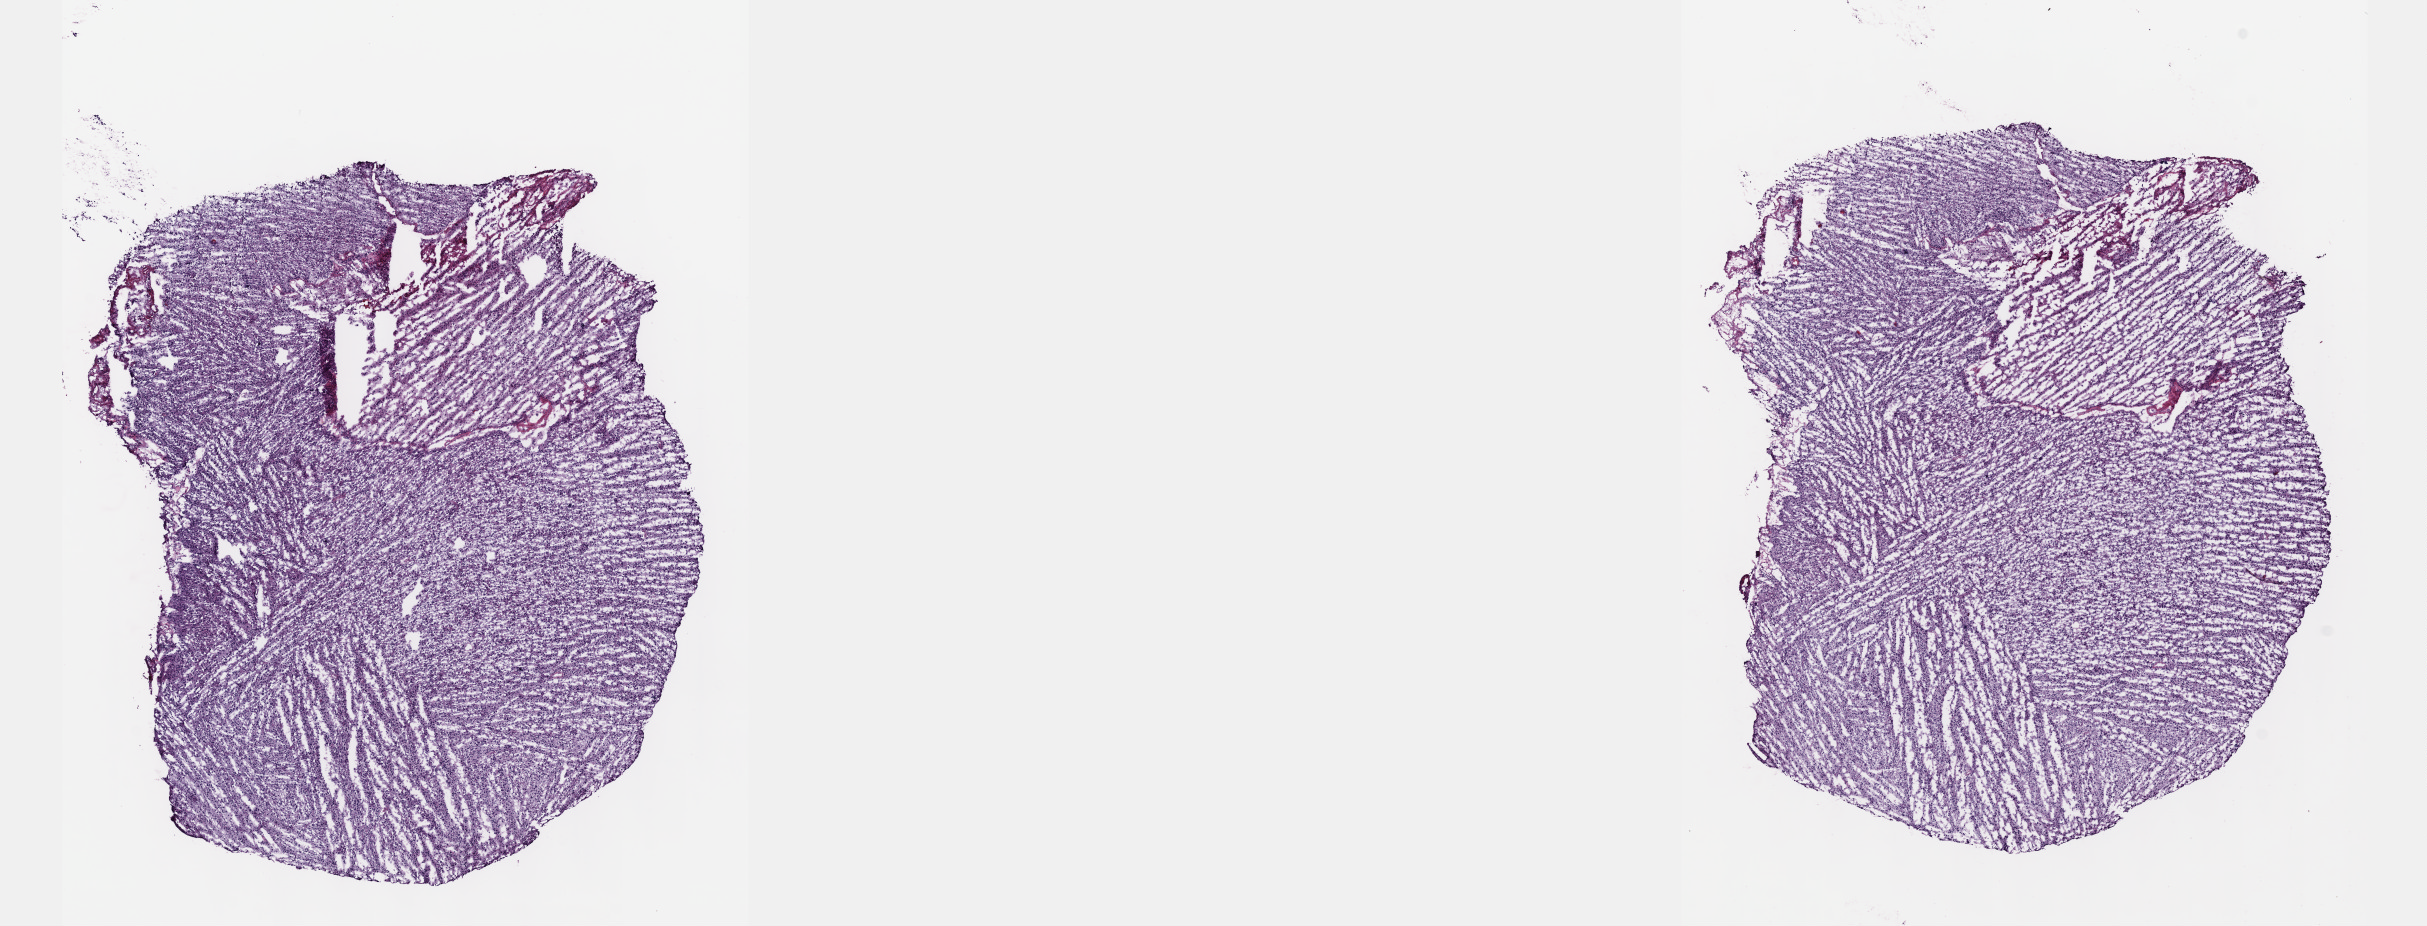
Whole-slide histology image, H&E — whole scanned area (about 19.6 x 7.5 mm) shown as a low-resolution overview, frozen section from the top of the tissue portion, sample: primary tumour, brain. Female, age 43 years at initial diagnosis. Histologic grade: G3 (poorly differentiated). Pathologist review of this section (percent, as recorded): tumour cells 65%, tumour nuclei 90%, normal cells 5%, stromal cells 30%, necrosis 0%. Infiltration values recorded for this section: lymphocyte infiltration 0%, monocyte infiltration 0%, neutrophil infiltration 0%.
• histologic diagnosis: Astrocytoma, anaplastic (cerebrum)